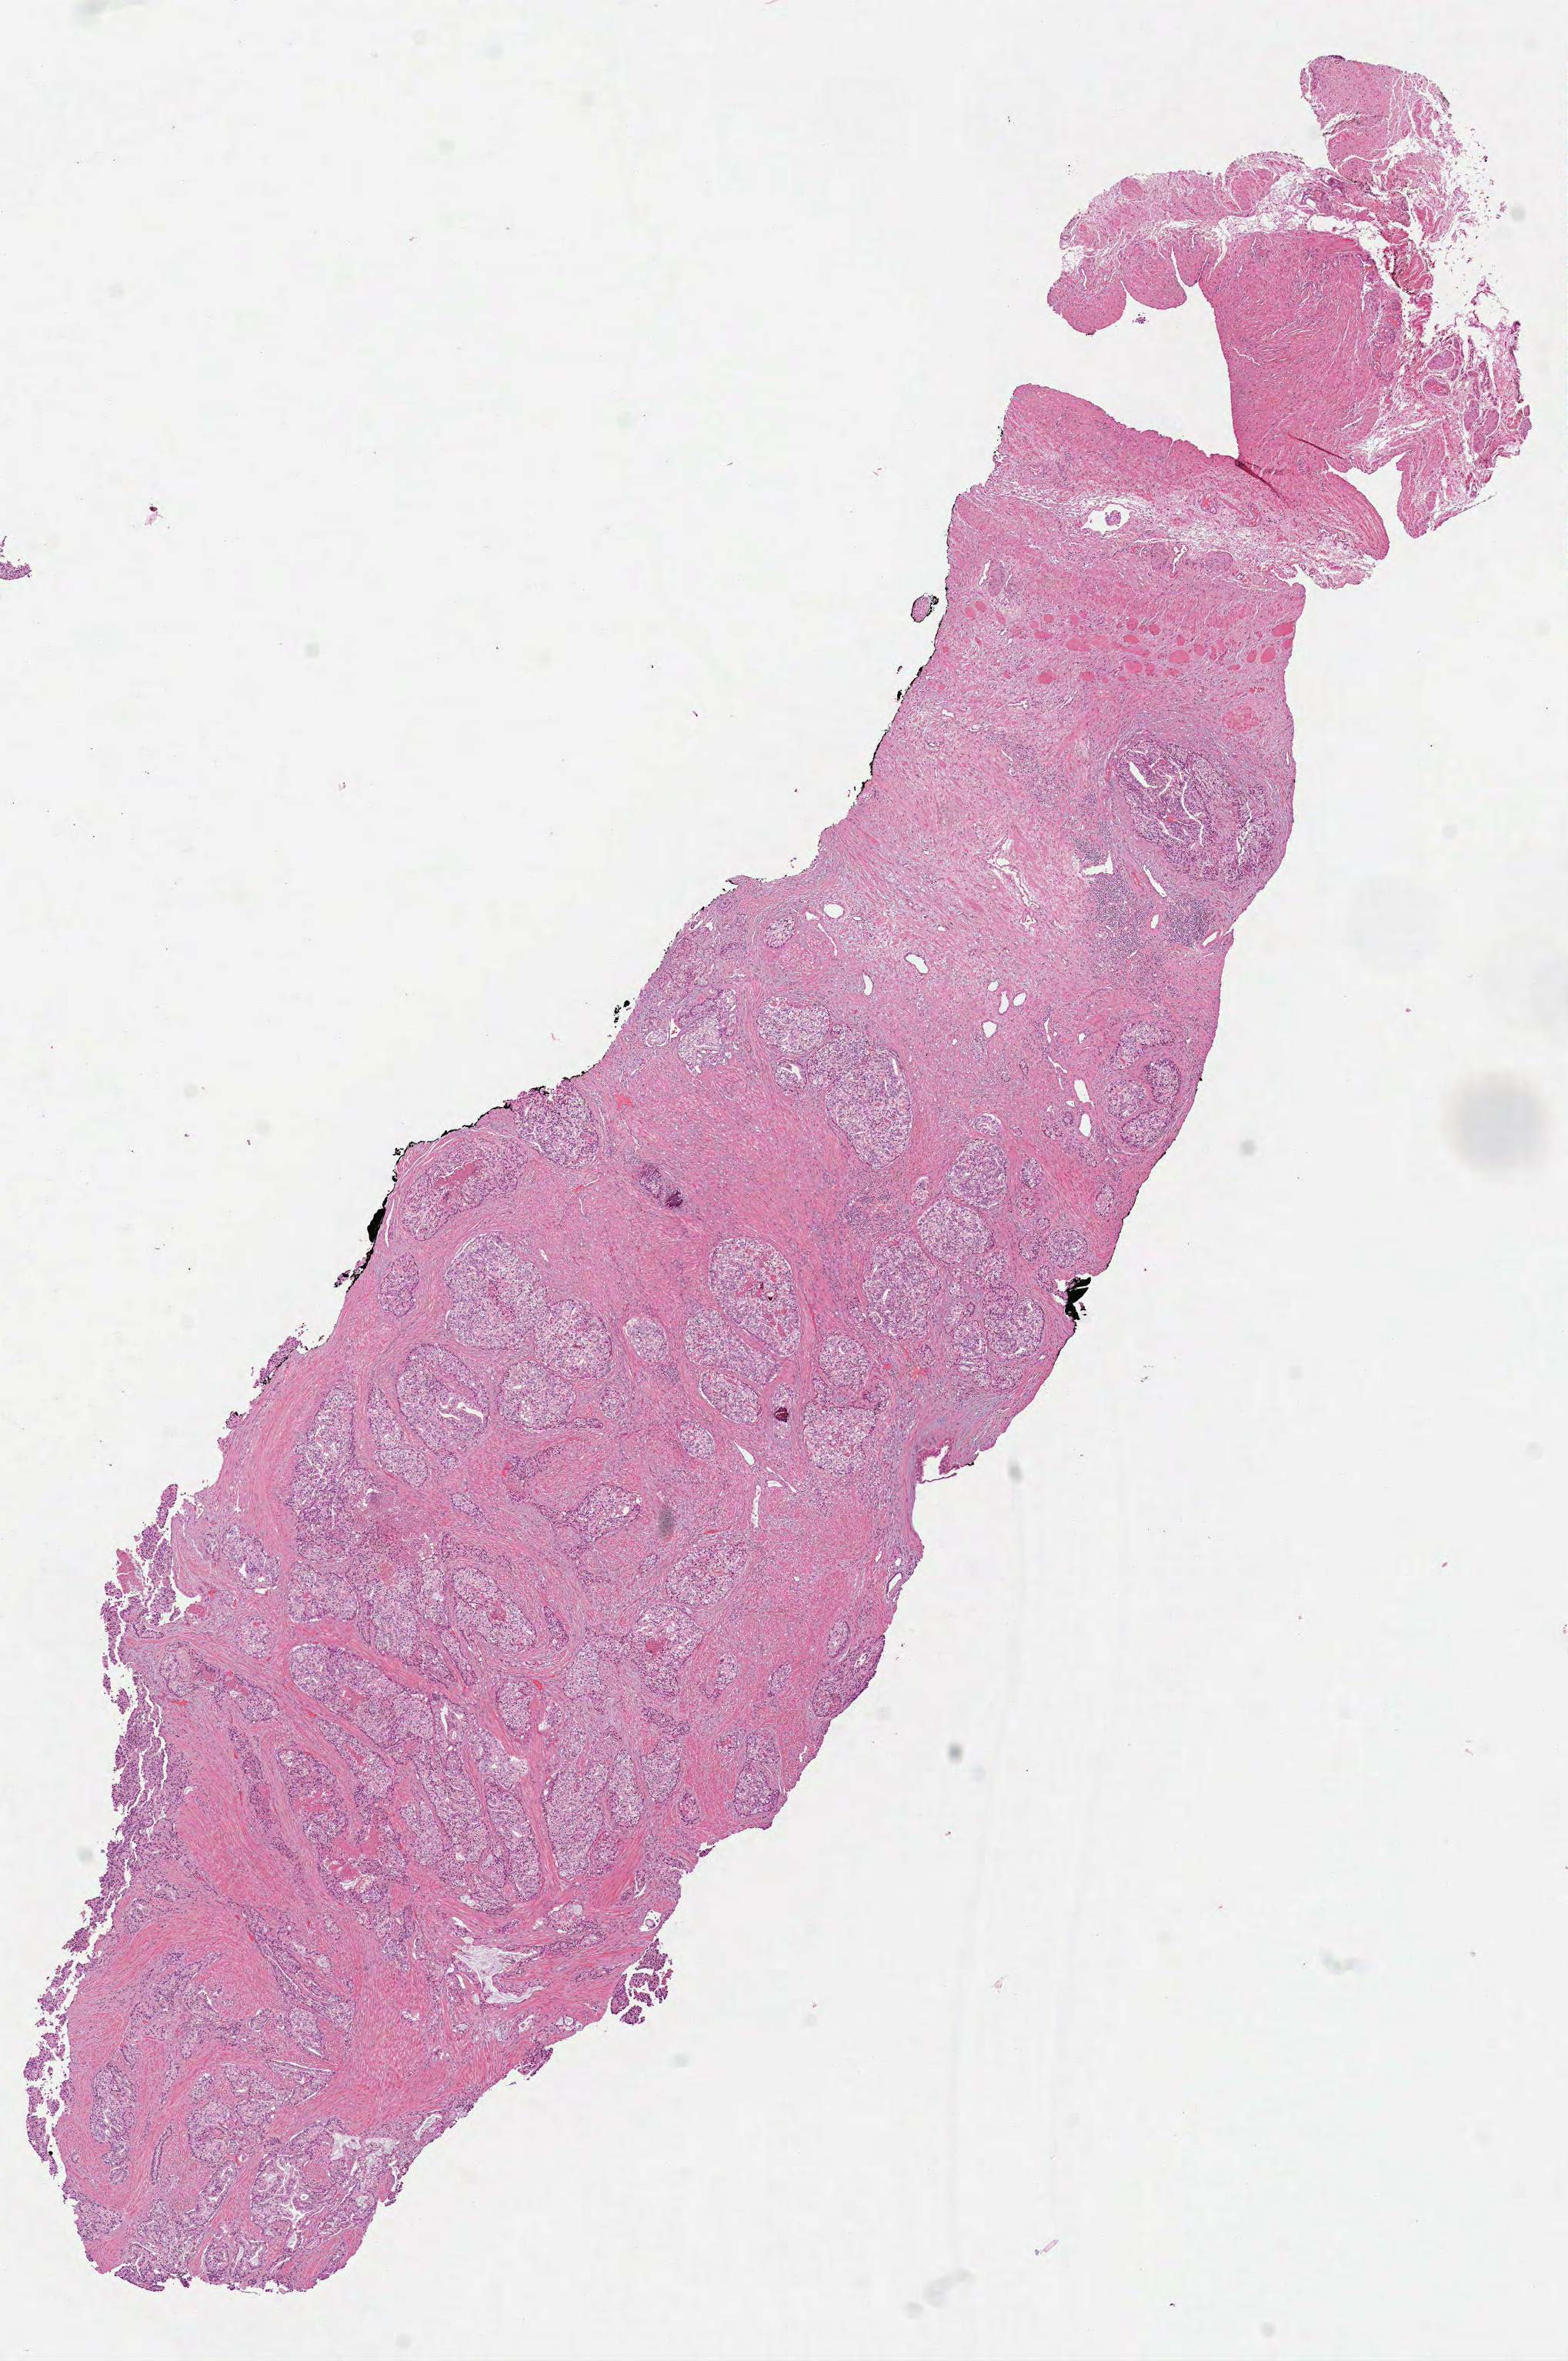
Digitized Hematoxylin and eosin (H&E) stained tissue section (whole slide), a low-resolution overview of the entire scanned area, about 8.2 x 12.4 mm. FFPE section. Sample: primary tumour, prostate. Patient: male, age at initial diagnosis 47 years. Gleason score: 8 (4+4).
Pathologic diagnosis: Adenocarcinoma, NOS (prostate gland). Laterality: bilateral. Lymph nodes positive (case pathology): 1 of 10 examined.